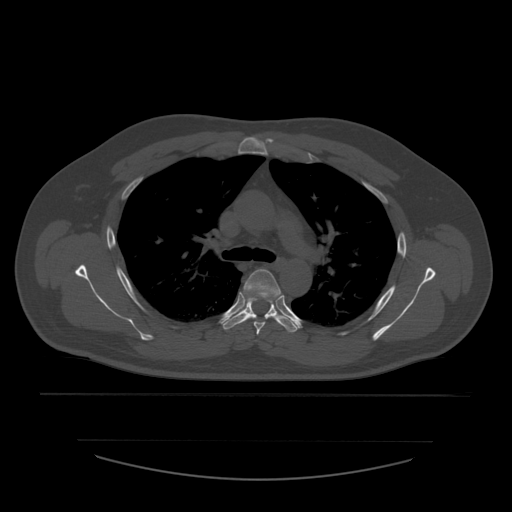
CT including the spine, one axial slice; slice 407 of 532 in the series (ordered by position); reconstruction kernel STANDARD; 120 kVp; bone window (W 1800 / L 400 HU); 1.25 mm slice thickness; 512 × 512 image matrix. Patient age 44 years. From the clinical record (not read from this slice): primary cancer: soft tissue sarcoma.
Annotated regions visible in this slice (semi-automatic segmentation, software-assisted and operator-edited):
- T4 vertebra: box from (x=244, y=269) to (x=282, y=335) px
- T5 vertebra: (x=223, y=301)–(x=298, y=333)